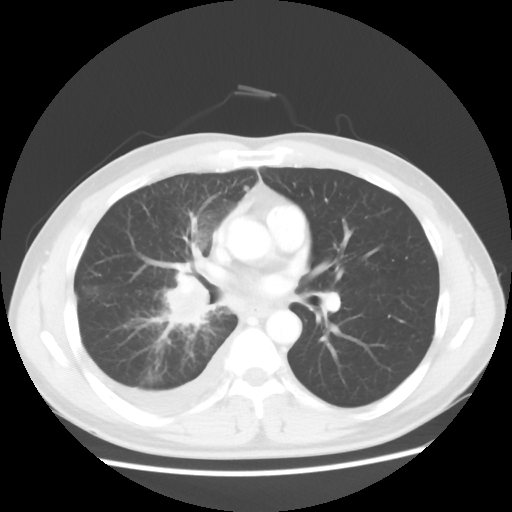
Chest CT, one axial slice. 120 kVp. Lung window (W 1500 / L -600 HU). 5 mm slice thickness. 512 × 512 image matrix. Male patient, age 46 years. From the clinical record (not read from this slice): clinical TNM (as recorded): T2 N3 M1.
Outlined on this slice (rectangle marked by the reading radiologist):
- lung tumour (recorded histology: adenocarcinoma): bounding box (x1, y1, x2, y2) in pixels: (157, 272, 205, 335)